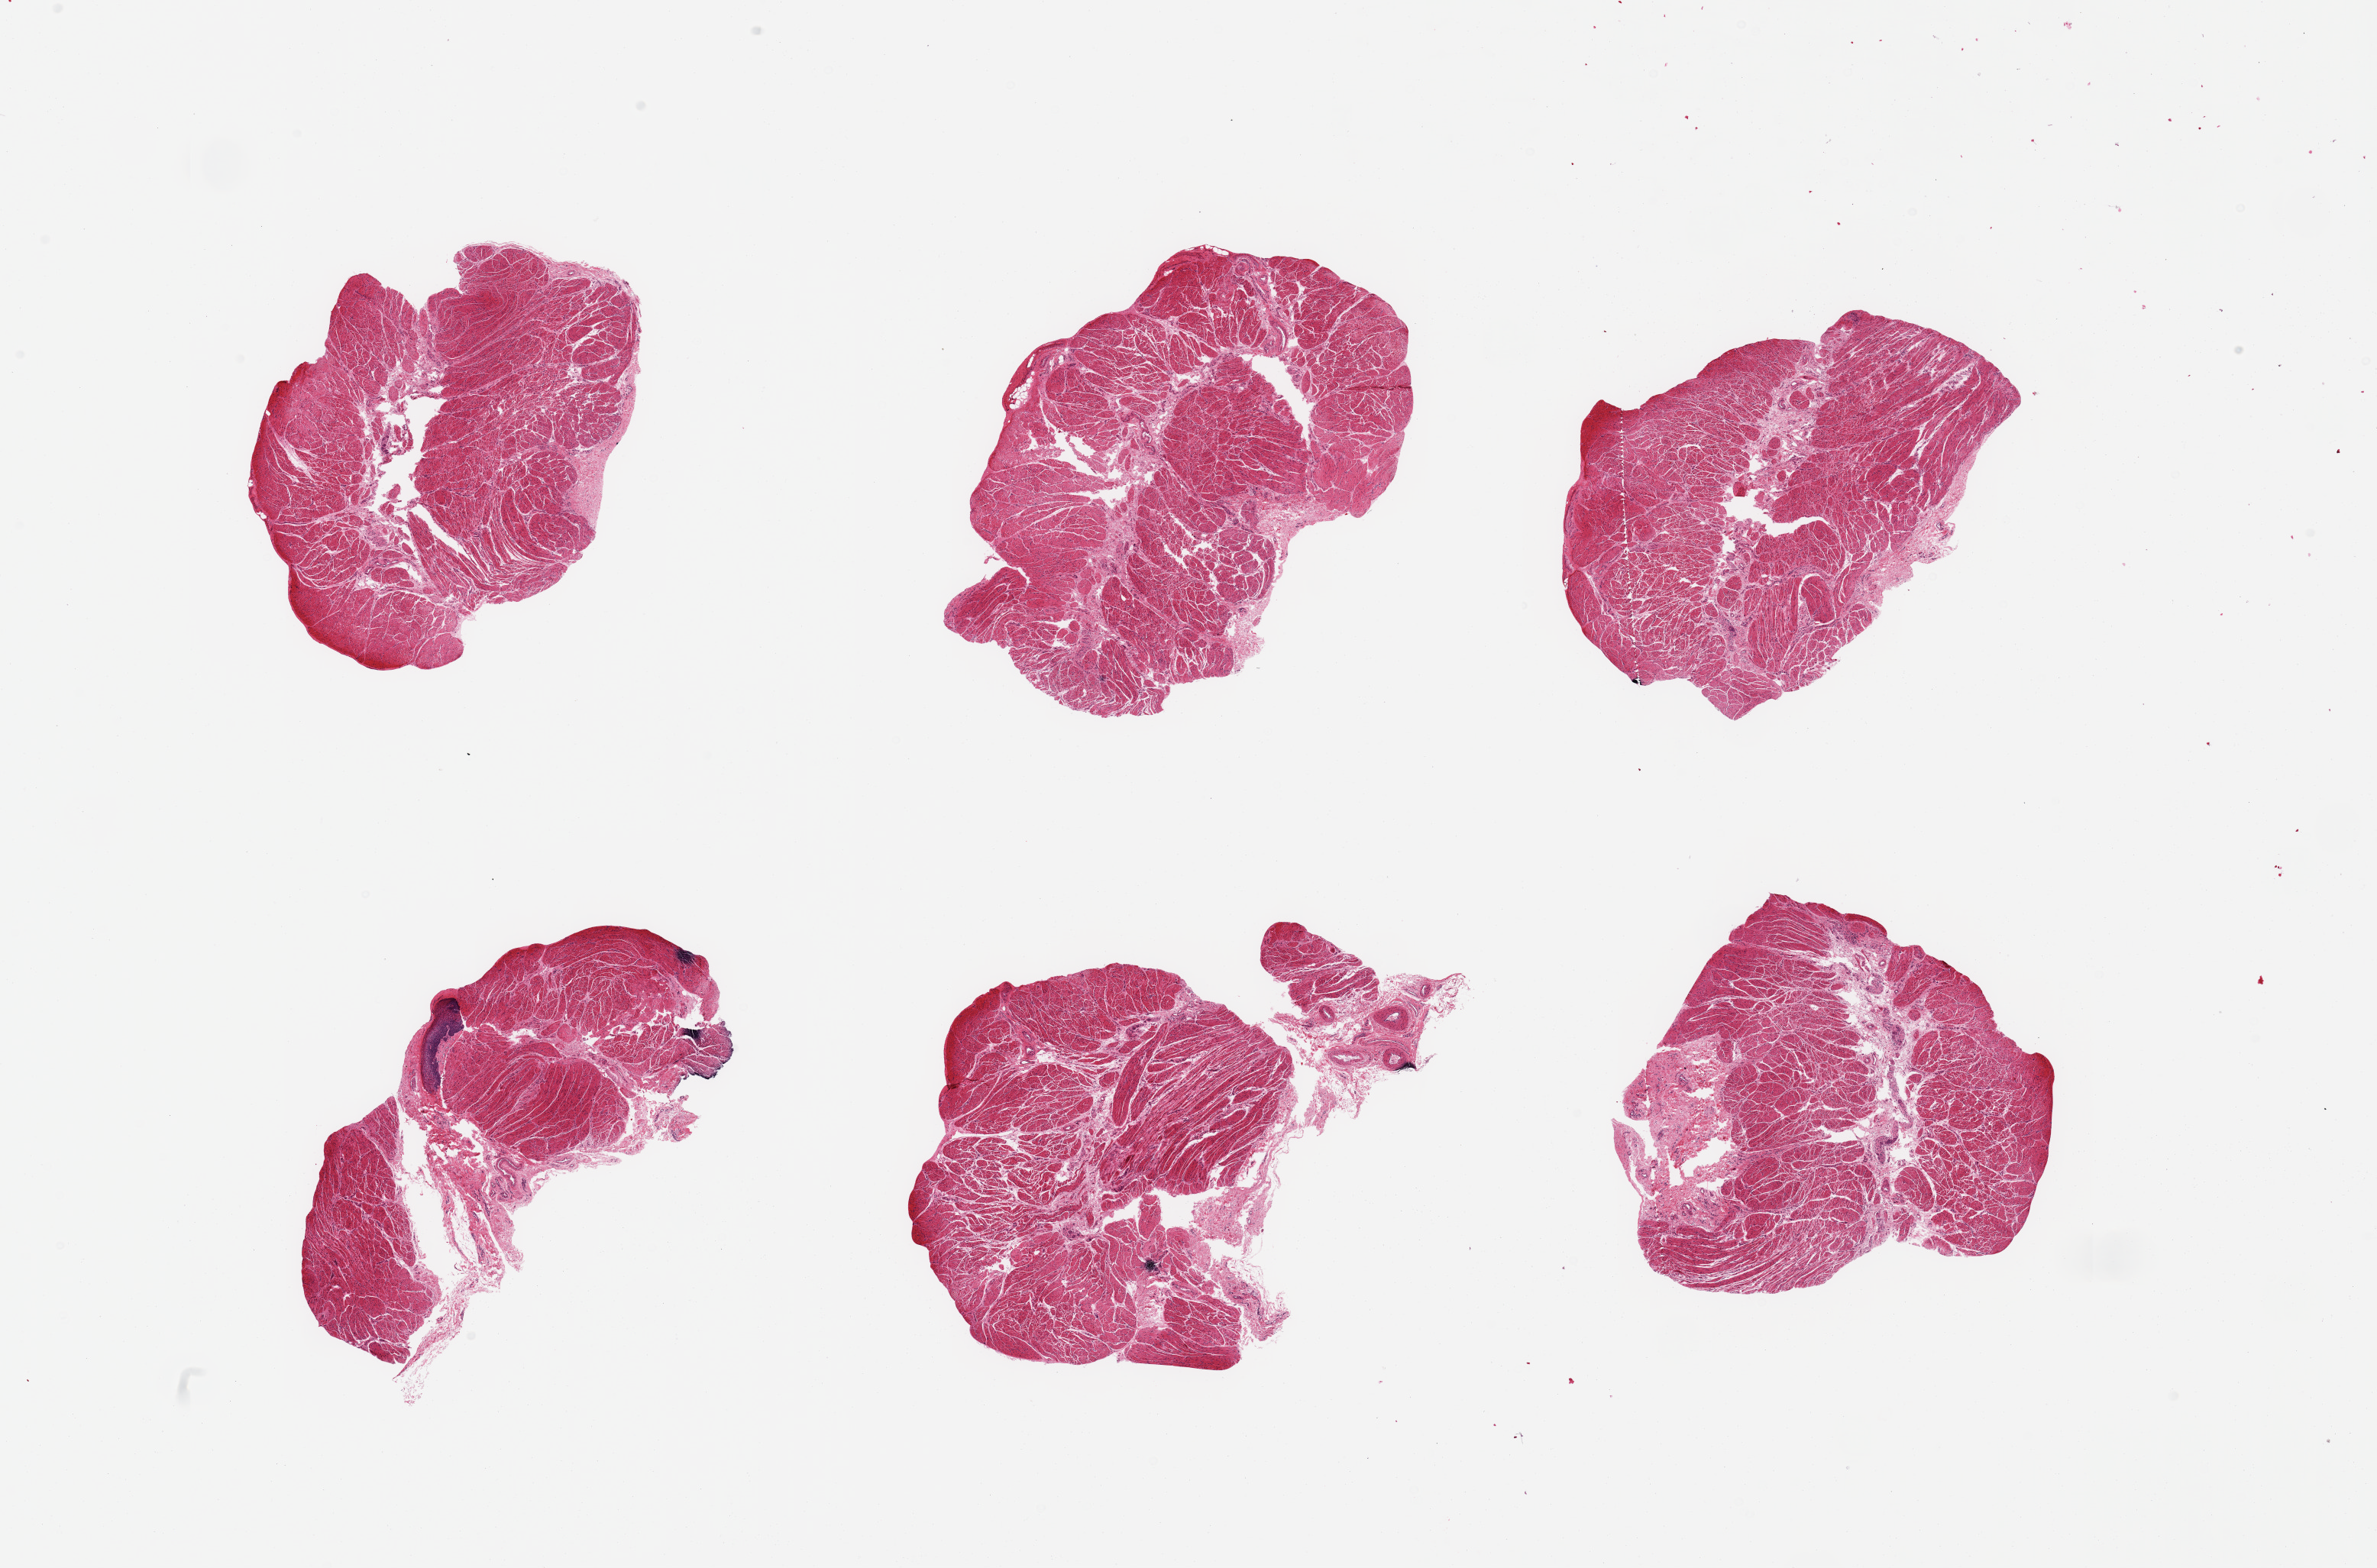
Whole-slide image, hematoxylin and eosin (H&E) stain, brightfield — low-resolution overview of the scanned area, about 24.6 x 16.2 mm (acquisition: 20x scan). PAXgene-fixed paraffin-embedded (PFPE) section. Target tissue: esophageal muscle. Tissue donor sample. Donor: male.
Pathologist's review note for this sample: 6 pieces, confirmed target muscularis.